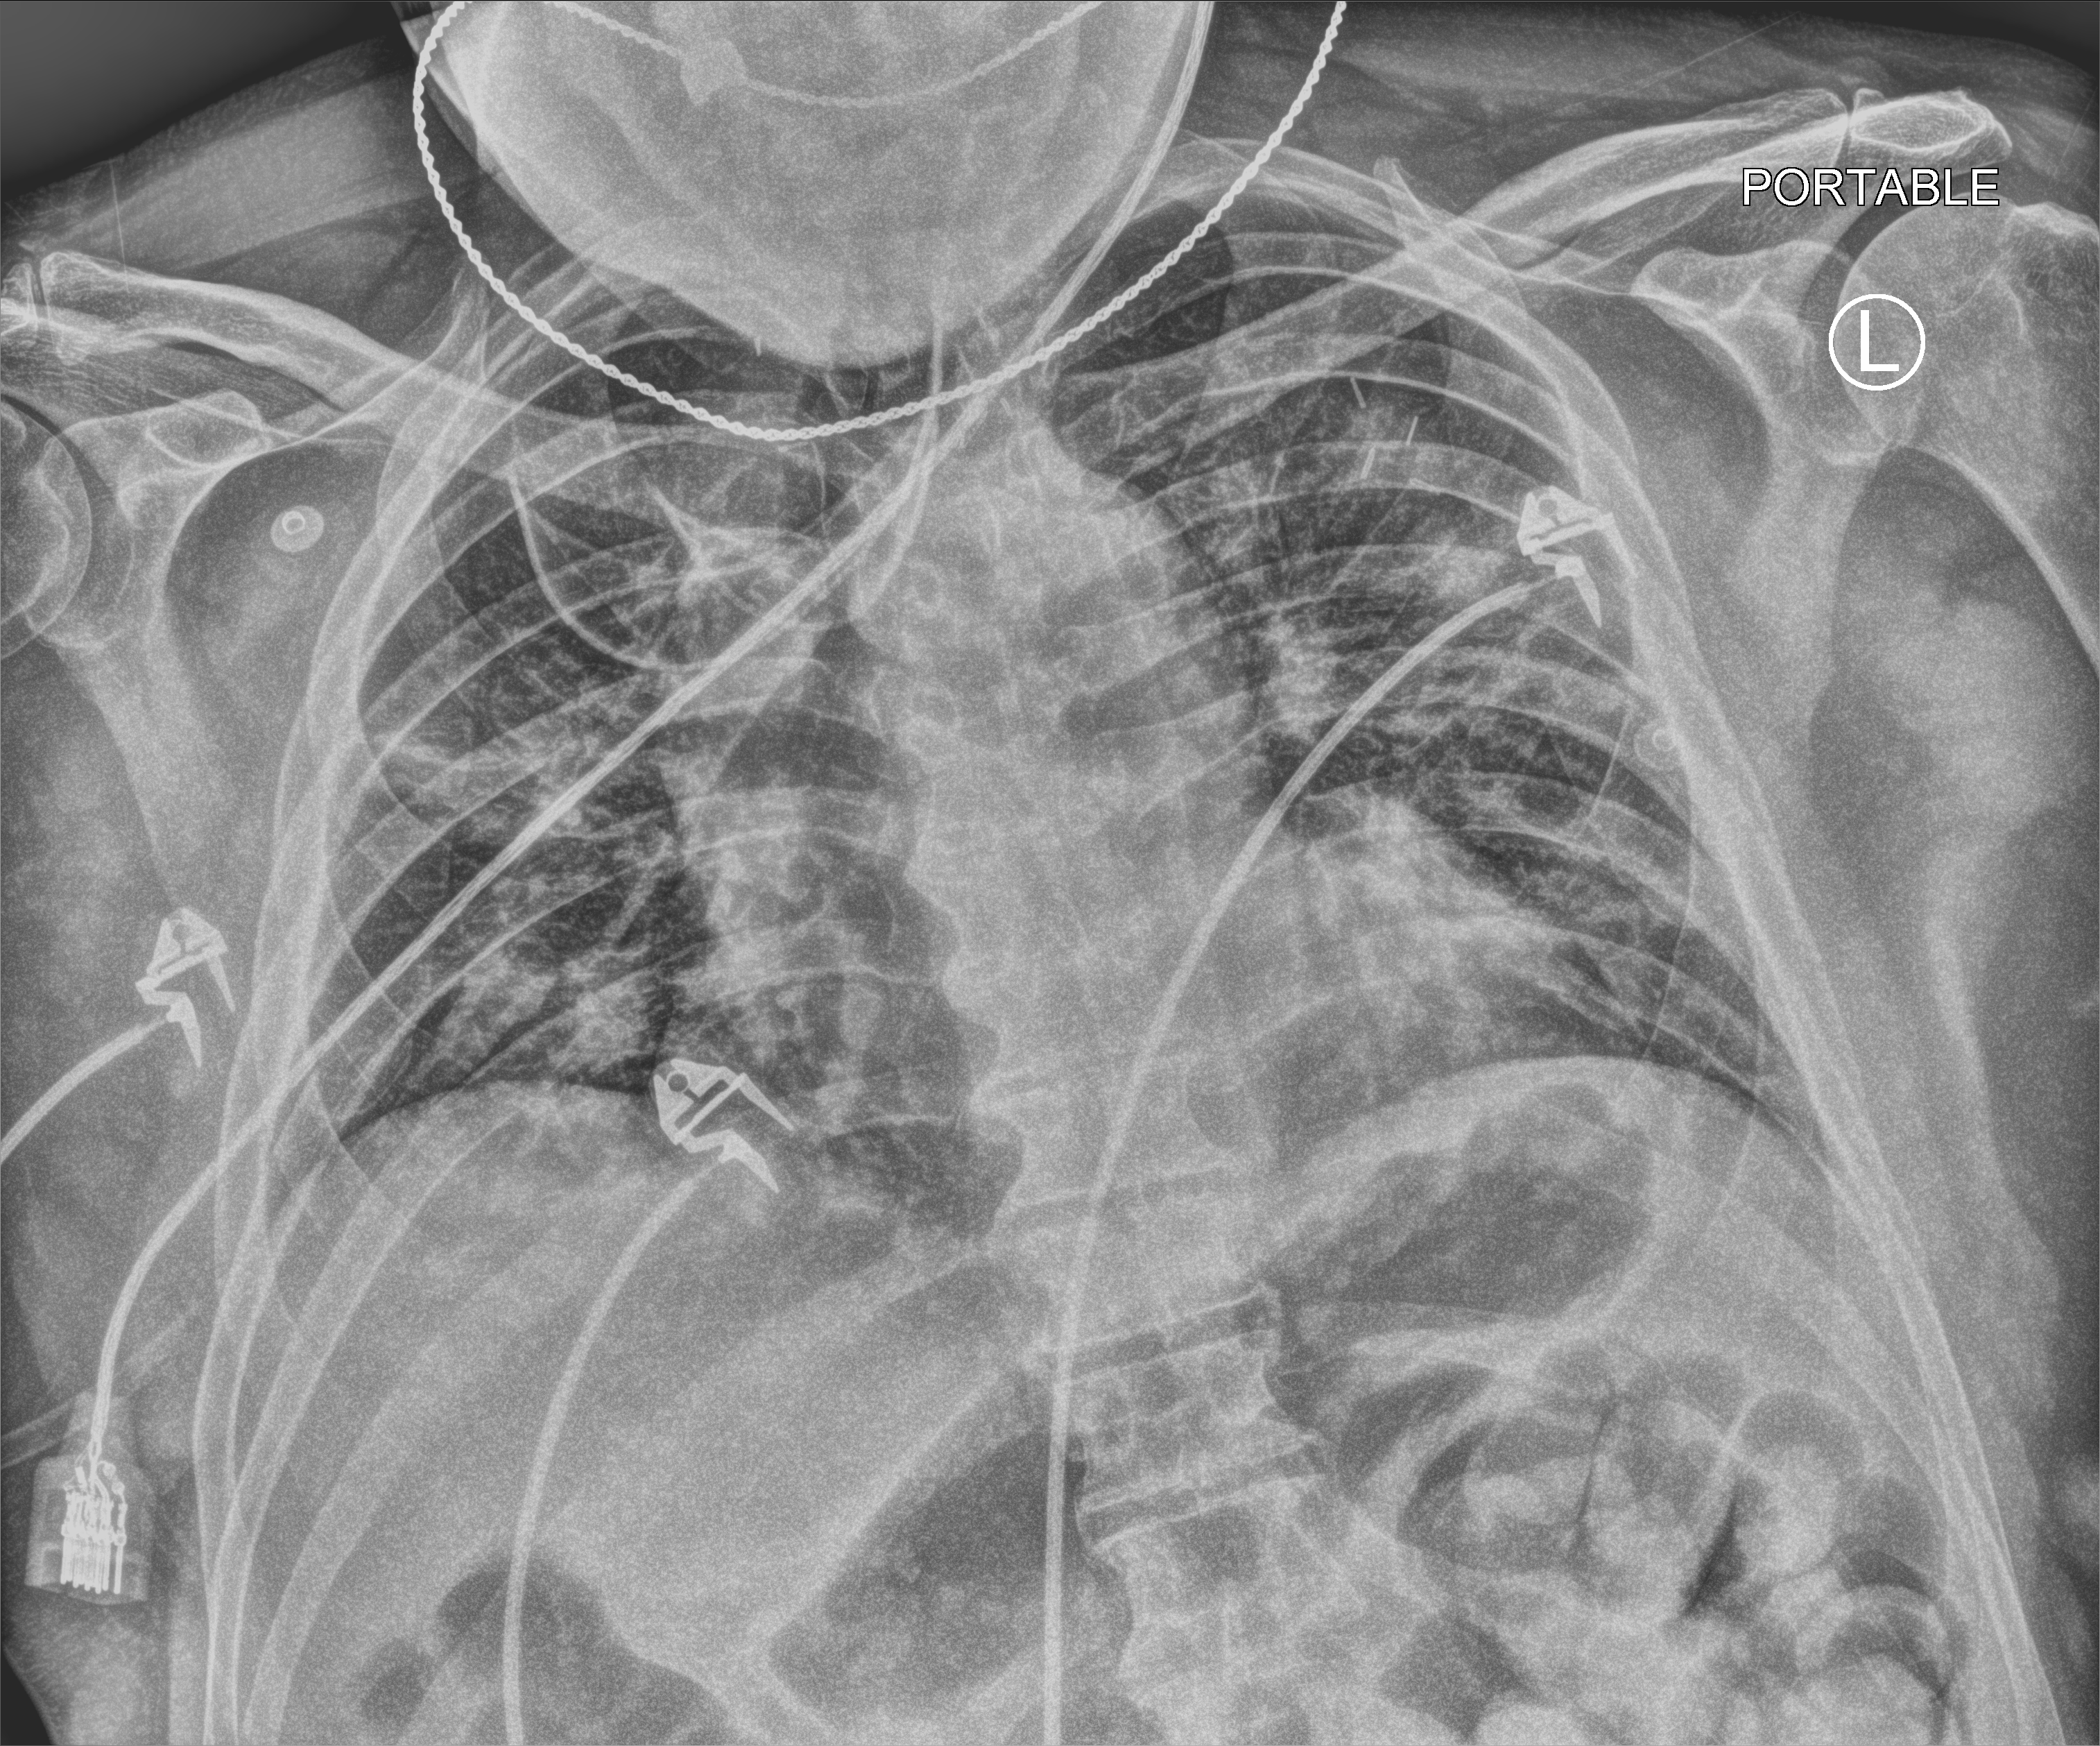
Chest X-ray (portable); anteroposterior (AP) projection. Adult patient hospitalised with COVID-19, age 18–59 years.
Hospital-stay facts (about this admission, not read from this image; timing relative to this image not recorded):
- admitted to intensive care during this hospital stay: yes
- length of hospital stay: 19 days
- mechanically ventilated during this hospital stay: yes